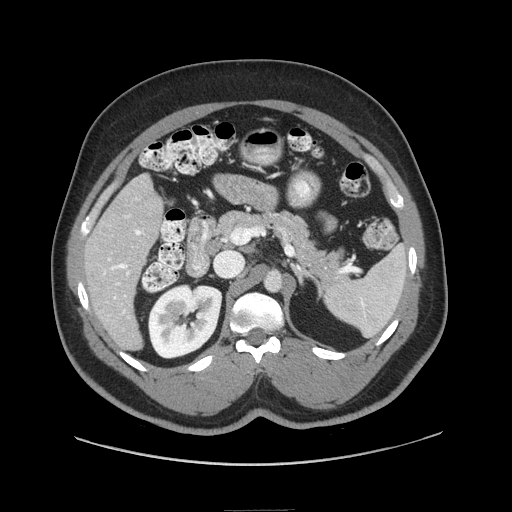
Contrast-enhanced abdominal CT (liver protocol), one axial slice. Position 36 of 87 along the scan axis. Reconstruction kernel STANDARD. 140 kVp. Soft-tissue window (W 400 / L 40 HU). 2.5 mm slice thickness. 512 × 512 image matrix, field of view 440 × 440 mm. Case-level facts recorded for this patient, not image findings: diagnosis: hepatocellular carcinoma (patient treated with transarterial chemoembolisation; whether this scan precedes or follows treatment is not stated here); TNM stage (as recorded): Stage-II; Child-Pugh class: A; tumour differentiation: moderately differentiated; tumour nodularity: uninodular.
Structures marked on this image (semi-automatic segmentation, software-assisted and operator-edited):
- liver parenchyma outside the tumour (the mass and vessels are separate outlines, so this box may not span the whole liver): bounding box [x1, y1, x2, y2] px = [84, 174, 164, 350]
- liver vessels: [103, 198, 144, 319]